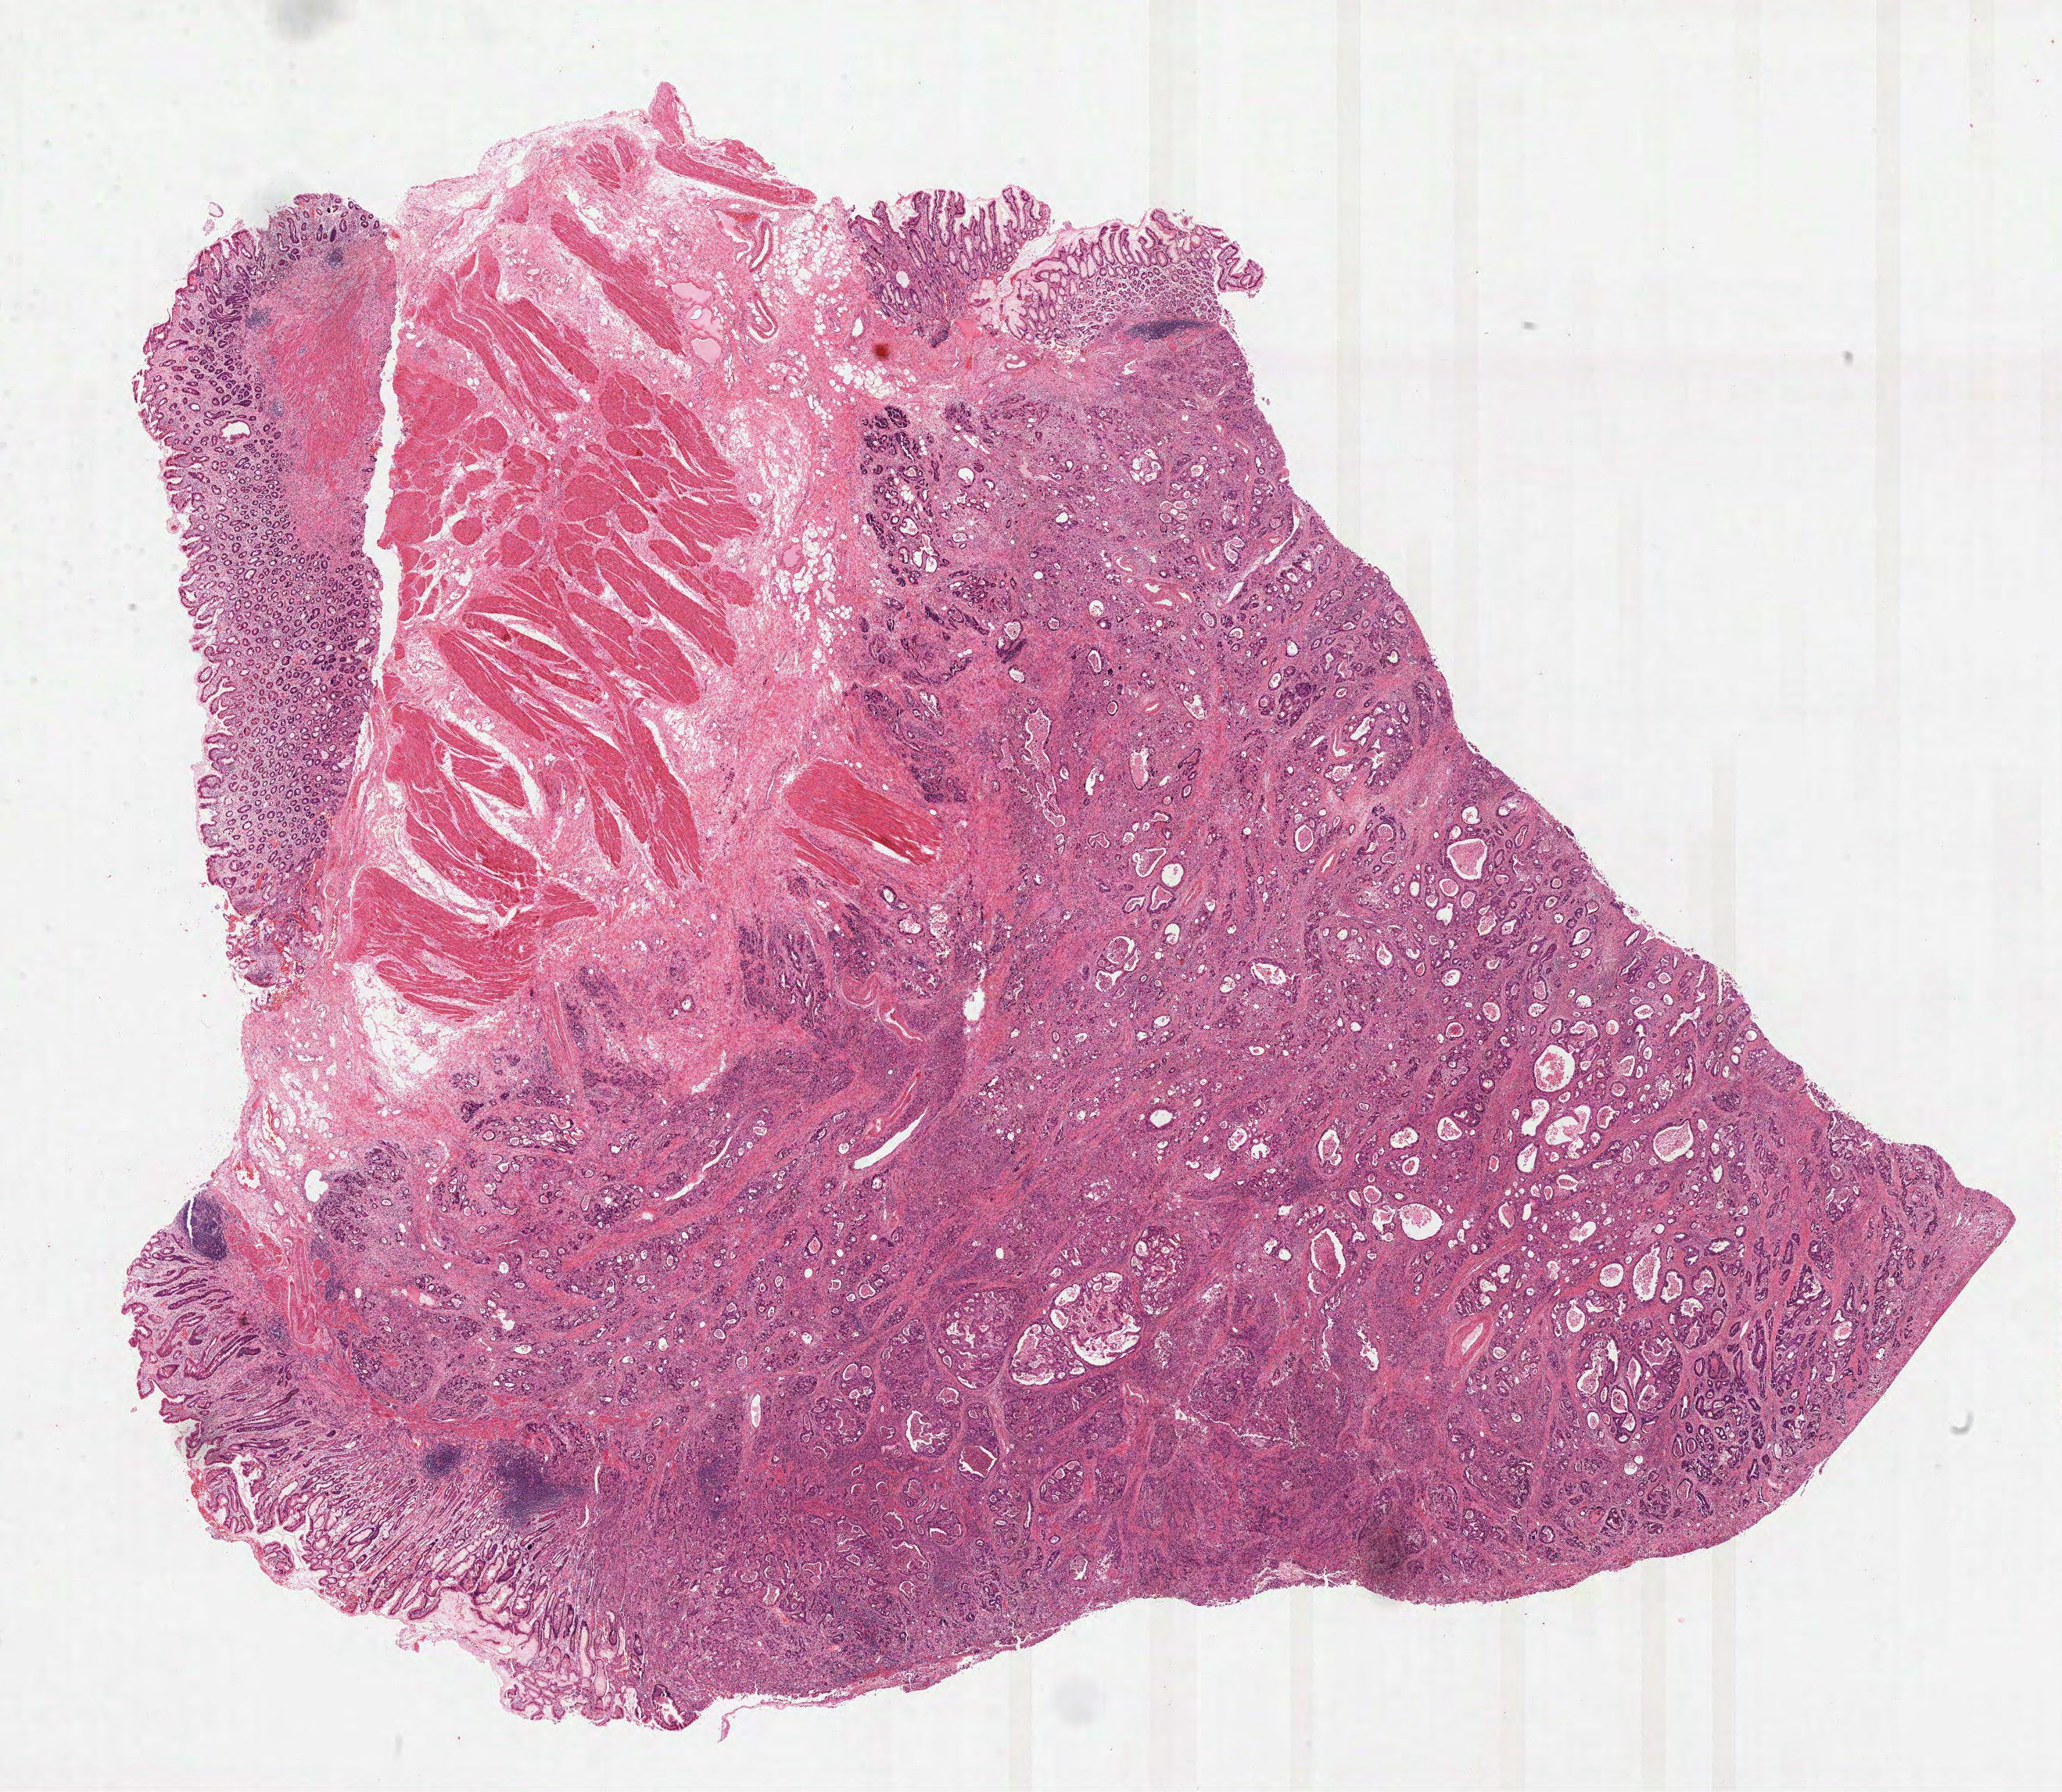
Whole-slide histology image, H&E, low-resolution overview of the scanned area, about 21.3 x 18.5 mm (from a 40x scan); FFPE section; primary tumour sample from the stomach. Male patient; age at initial diagnosis 61 years. Histologic grade: G2 (moderately differentiated).
AJCC pathologic stage: IIIA (7th edition). Lymph nodes positive (case pathology): 2 of 7 examined. Pathologic diagnosis: Adenocarcinoma, NOS (fundus of stomach).